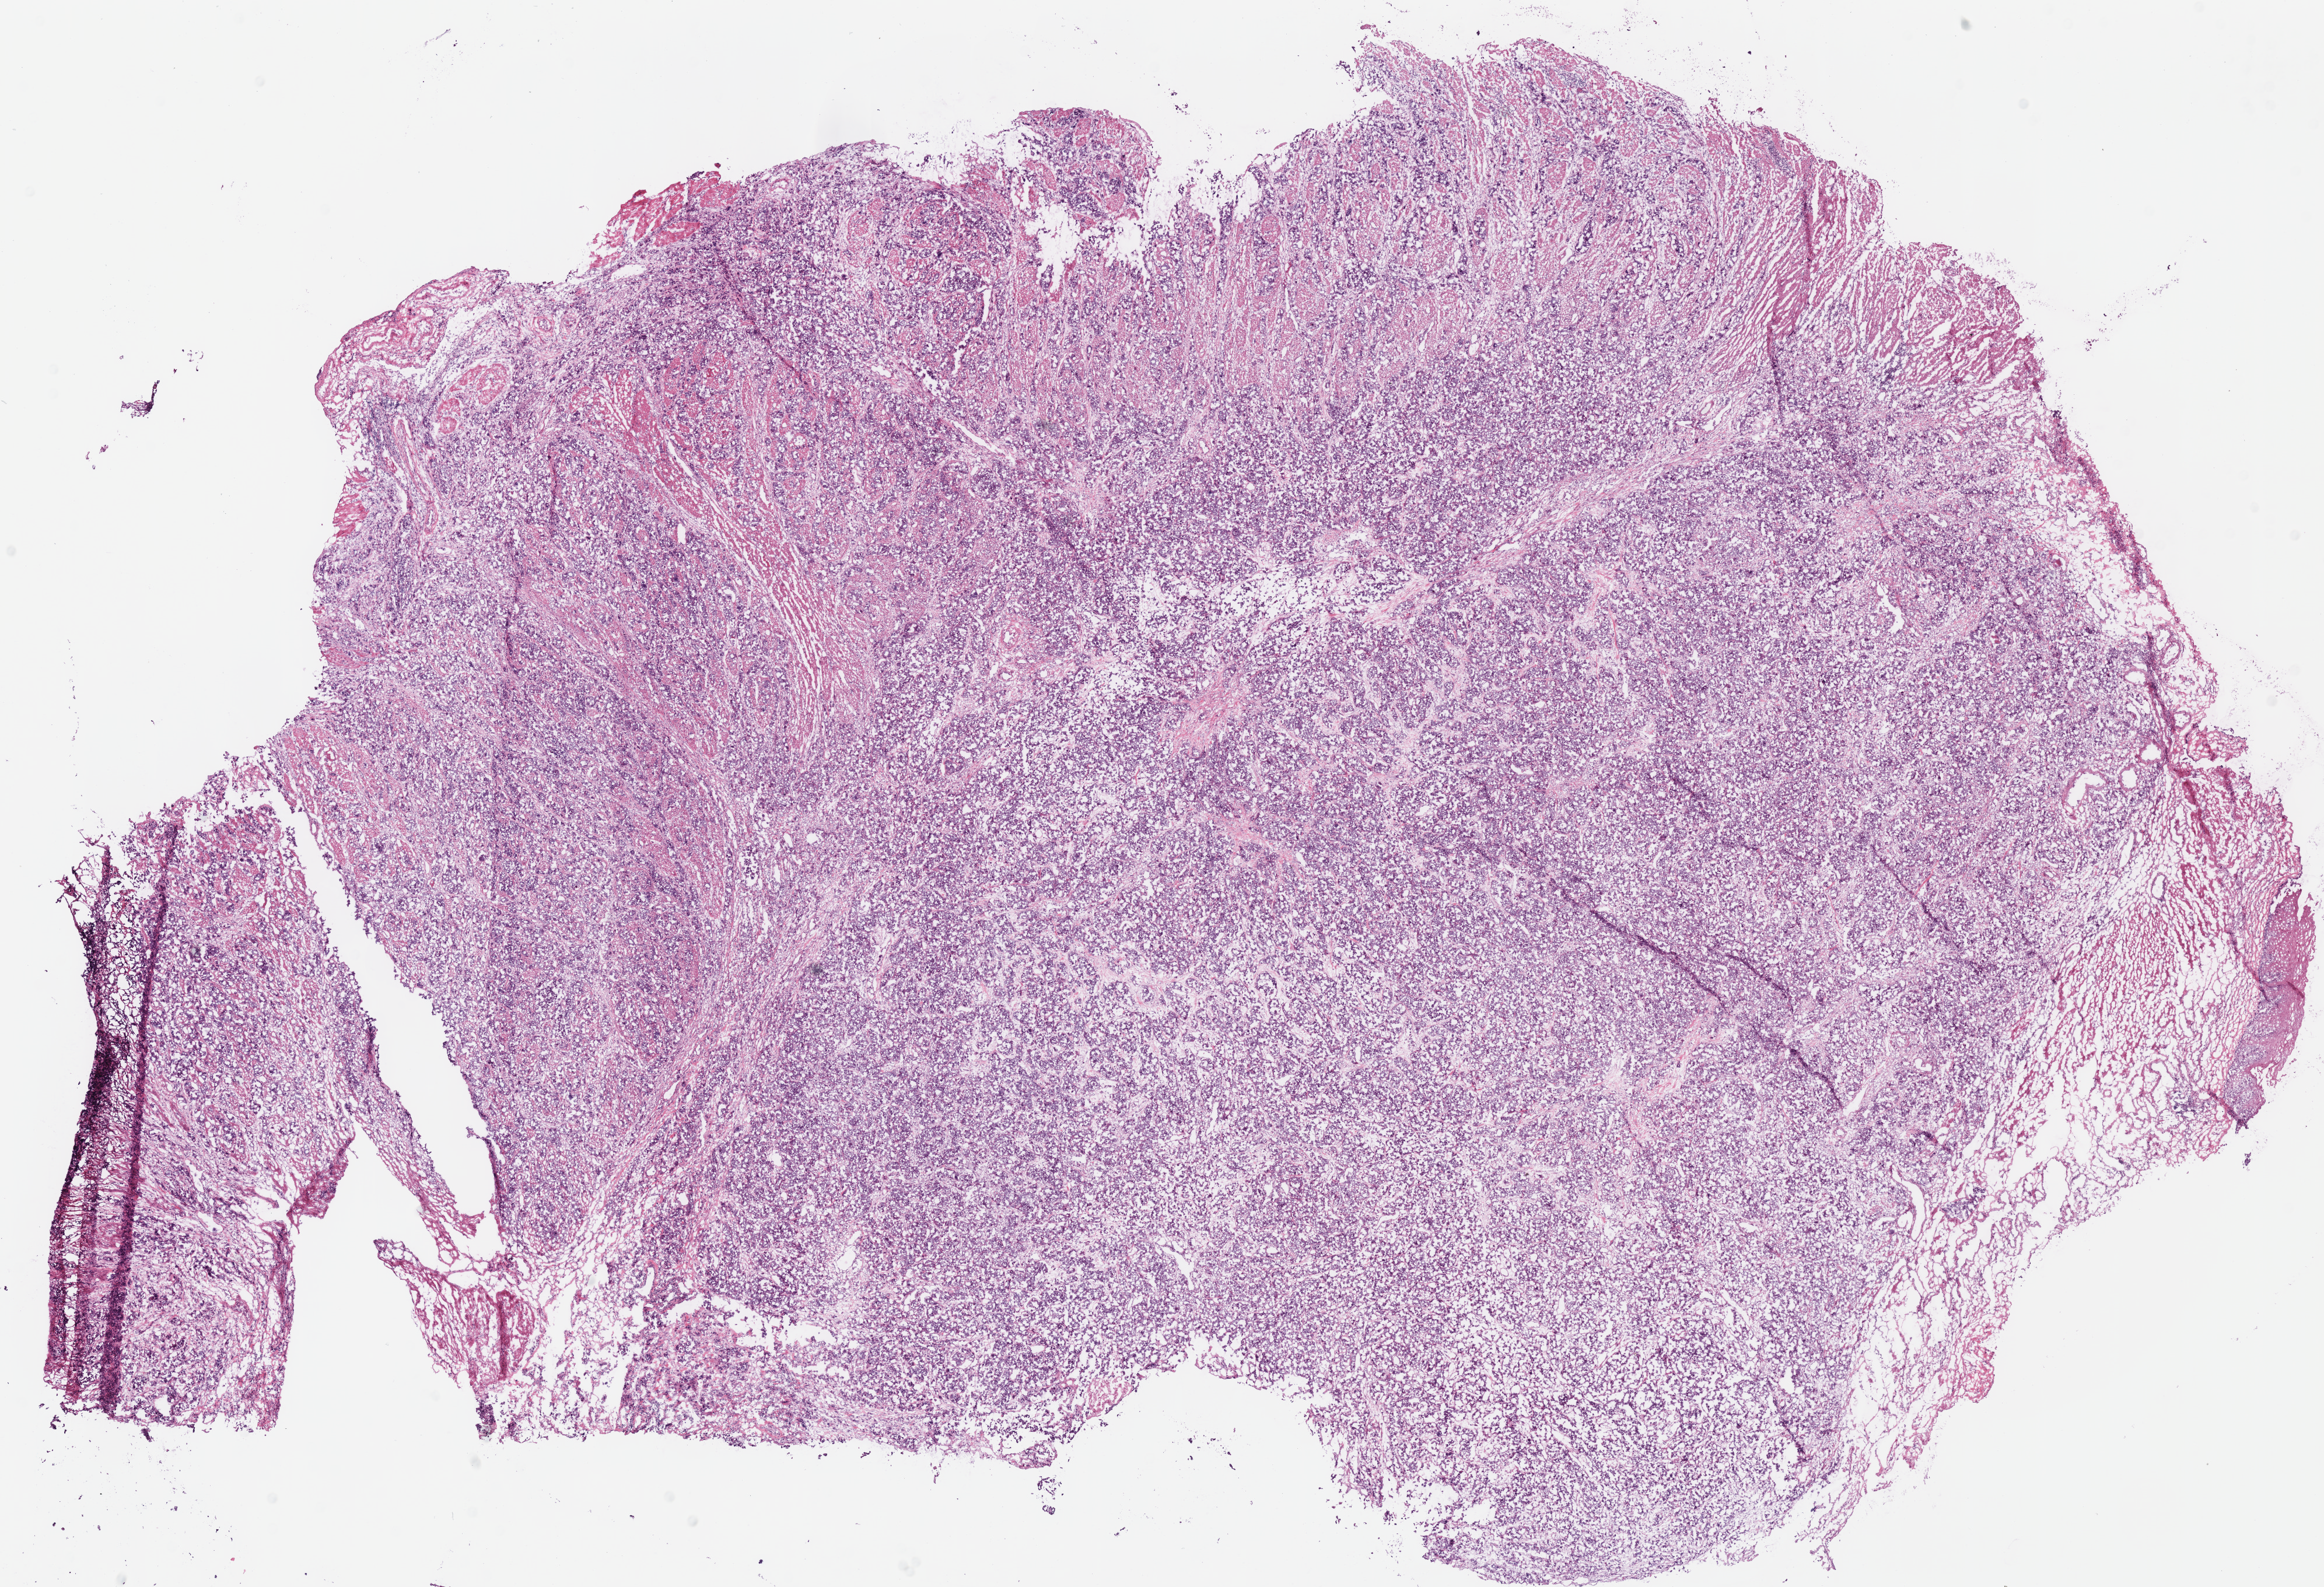
Hematoxylin and eosin (H&E) stained whole-slide image, low-resolution overview of the scanned area, about 15.7 x 10.7 mm (from a 40x scan); frozen section from the top of the tissue portion; sample: primary tumour, stomach. Male patient; age at initial diagnosis 68 years. Histologic grade: G3 (poorly differentiated). Slide review estimates, as recorded: tumour cells 95%, tumour nuclei 90%, normal cells 0%, stromal cells 5%, necrosis 0%.
AJCC pathologic stage: IIB (7th edition). Lymph nodes positive (case pathology): 9 of 14 examined. Histologic diagnosis: Adenocarcinoma, NOS (cardia, NOS).